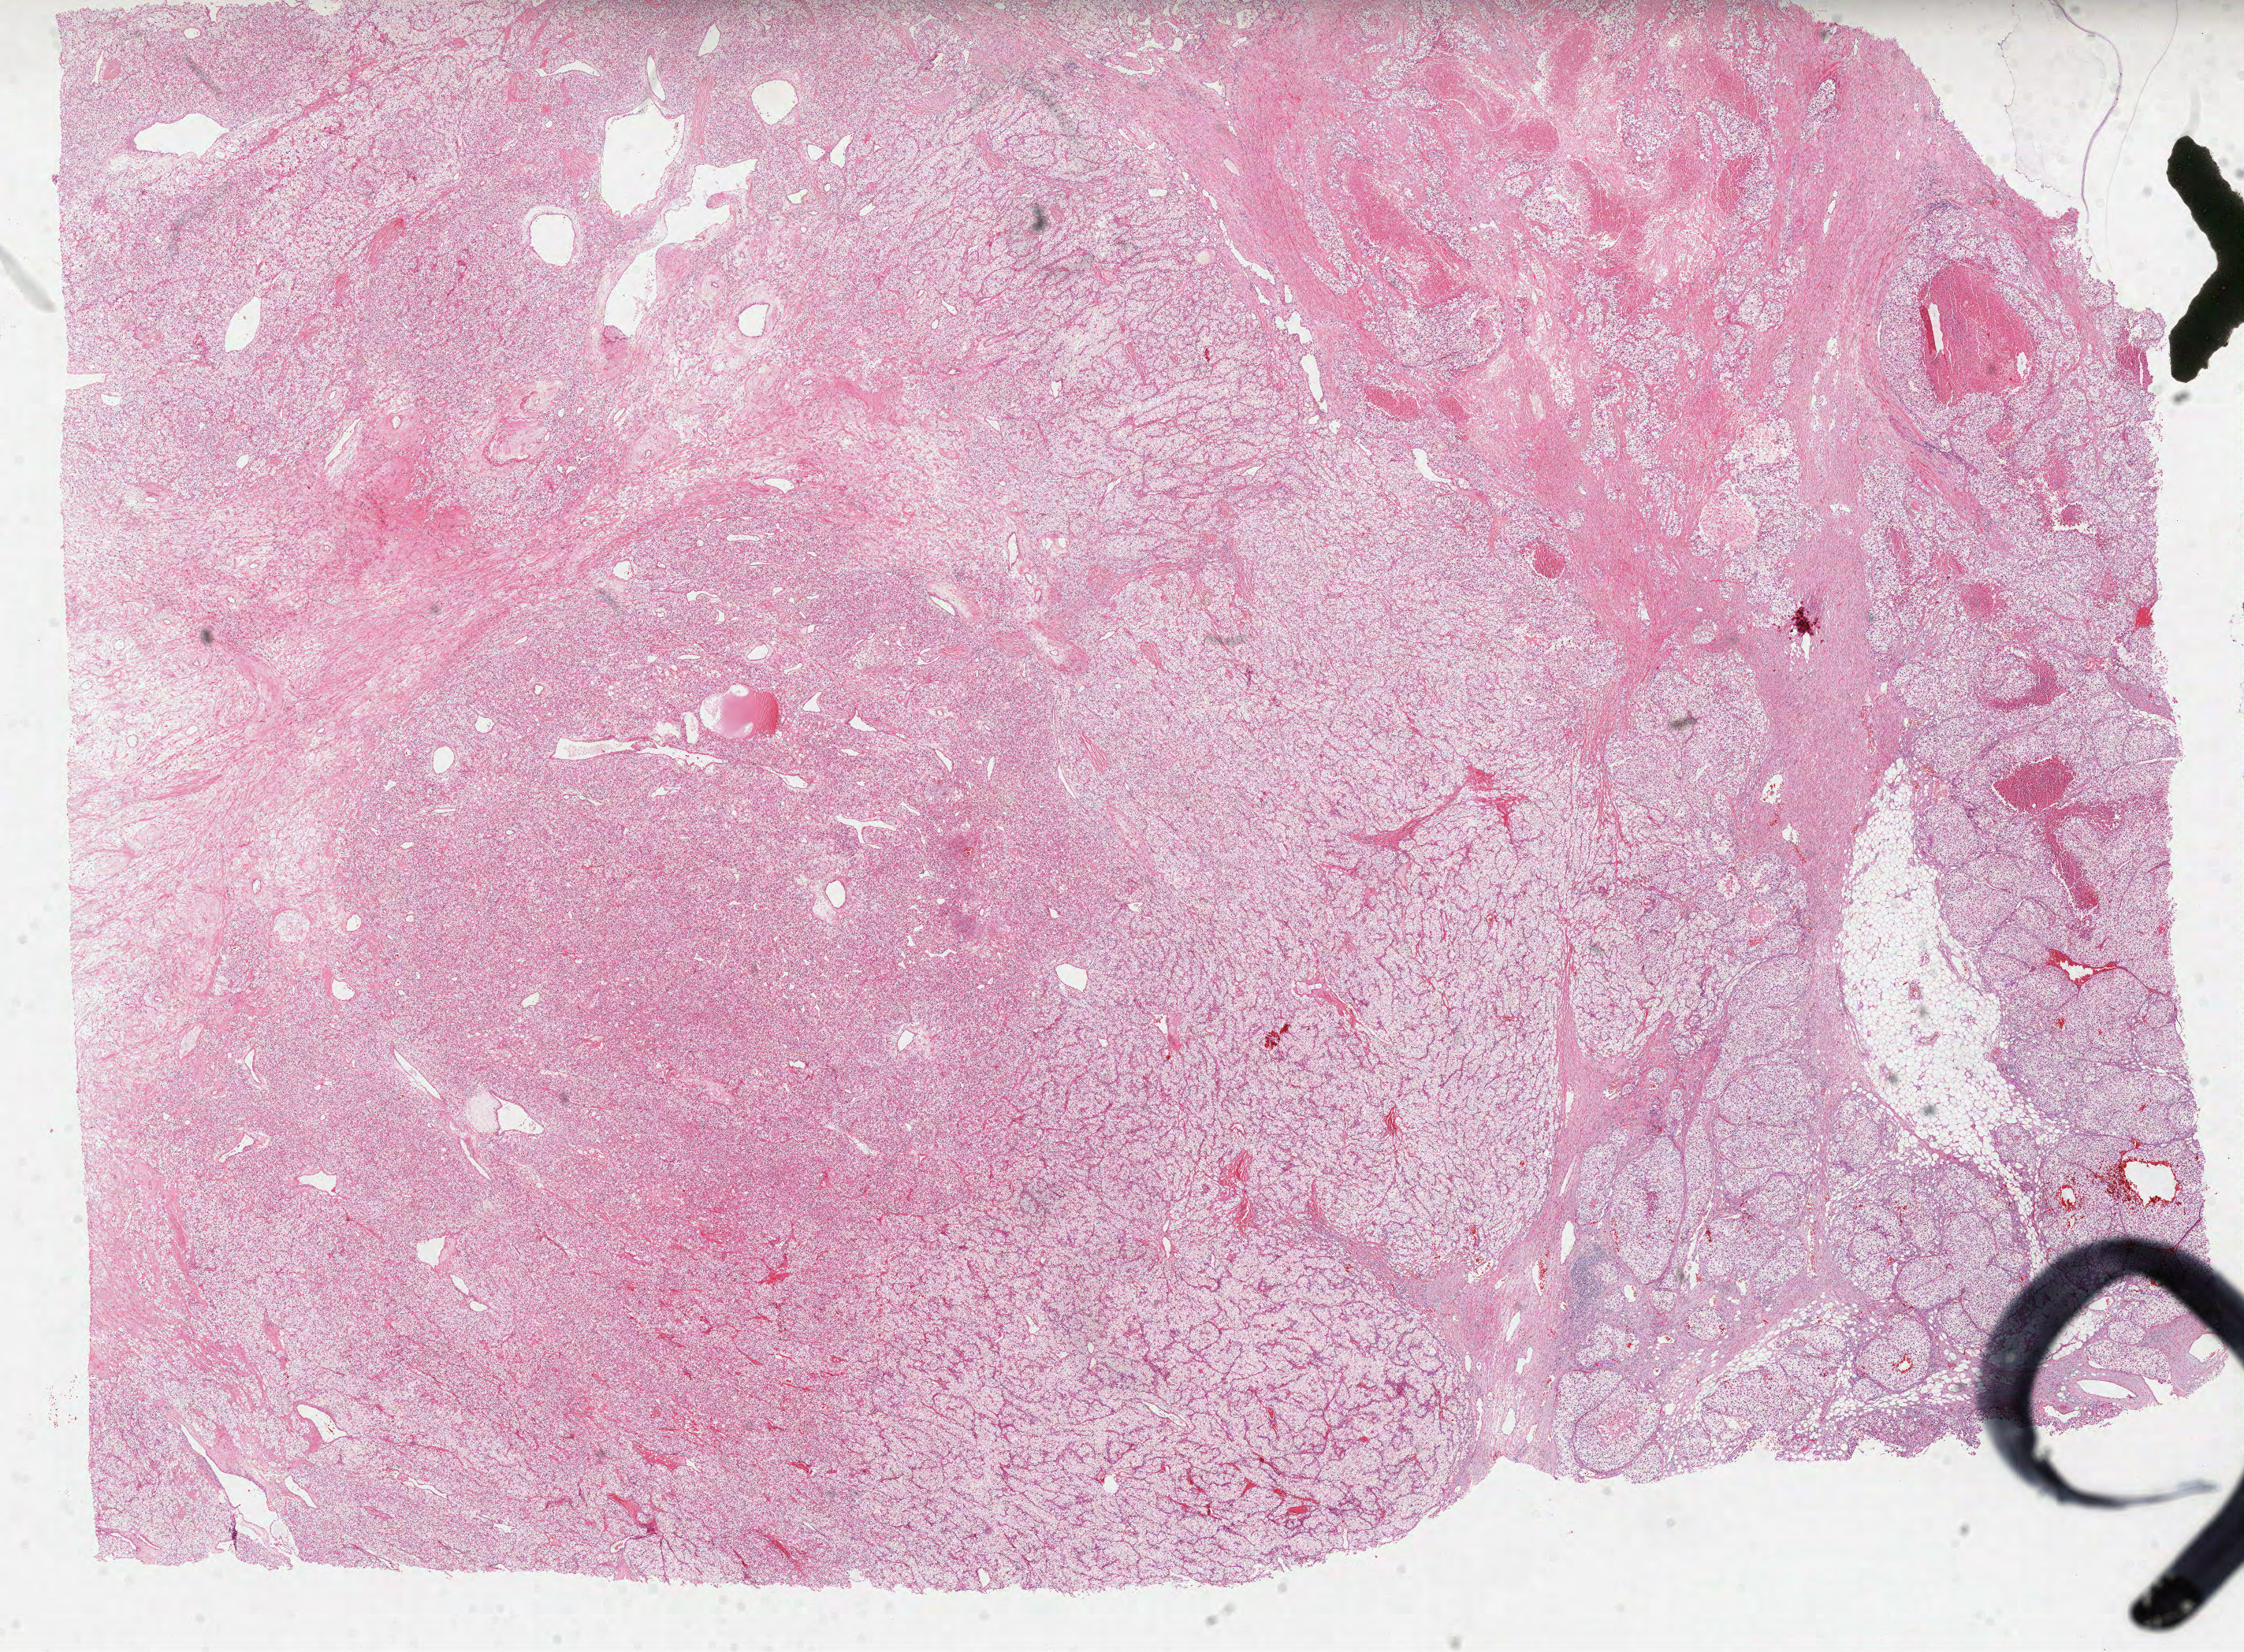
Digitized H&E-stained tissue section (whole slide), a low-resolution overview of the entire scanned area, about 23.0 x 16.9 mm; formalin-fixed paraffin-embedded (FFPE) diagnostic section; primary tumour sample from the kidney. Patient: male, age at initial diagnosis 60 years. Histologic grade: G3 (poorly differentiated).
* histologic diagnosis: Clear cell adenocarcinoma, NOS
* AJCC pathologic stage: IV
* TNM: T3a NX M1
* laterality: left